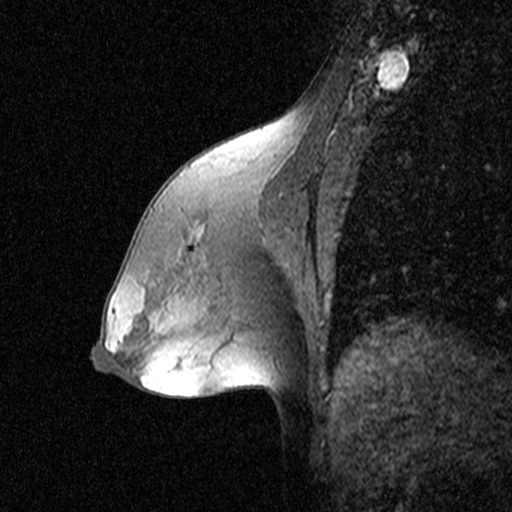
Breast MRI (dynamic contrast-enhanced), one sagittal slice; position 25 of 44 along the scan axis; dynamic contrast-enhanced study with each time point stored as its own series, time point 2 of 3 at this slice position (early post-contrast, ordered by acquisition time); 1.5 T; TE 4.5 ms, TR 11 ms; 3 mm slice thickness; 512 × 512 image matrix, field of view 200 × 200 mm. Patient: female, 53 years. From the clinical record (not read from this slice): setting: breast cancer imaged before/during neoadjuvant chemotherapy; receptor status: HR-positive, HER2-negative.
Outlined on this slice (semi-automatically segmented with operator editing):
- analysis volume of interest (the breast-tissue region the enhancement analysis was run in; not a lesion): bounding box [x1, y1, x2, y2] px = [176, 178, 299, 305]
- tumour enhancement mask (voxels above the 90 % enhancement threshold inside the analysis volume of interest): [198, 230, 201, 236]